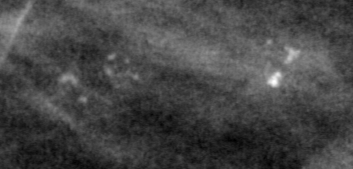
Crop from a digitized film mammogram around one marked abnormality; right breast; CC view; BI-RADS breast density category 2 (scale 1–4).
Calcifications, morphology pleomorphic, distribution clustered; BI-RADS assessment category 4; pathology result (as recorded, not read from the image): benign.